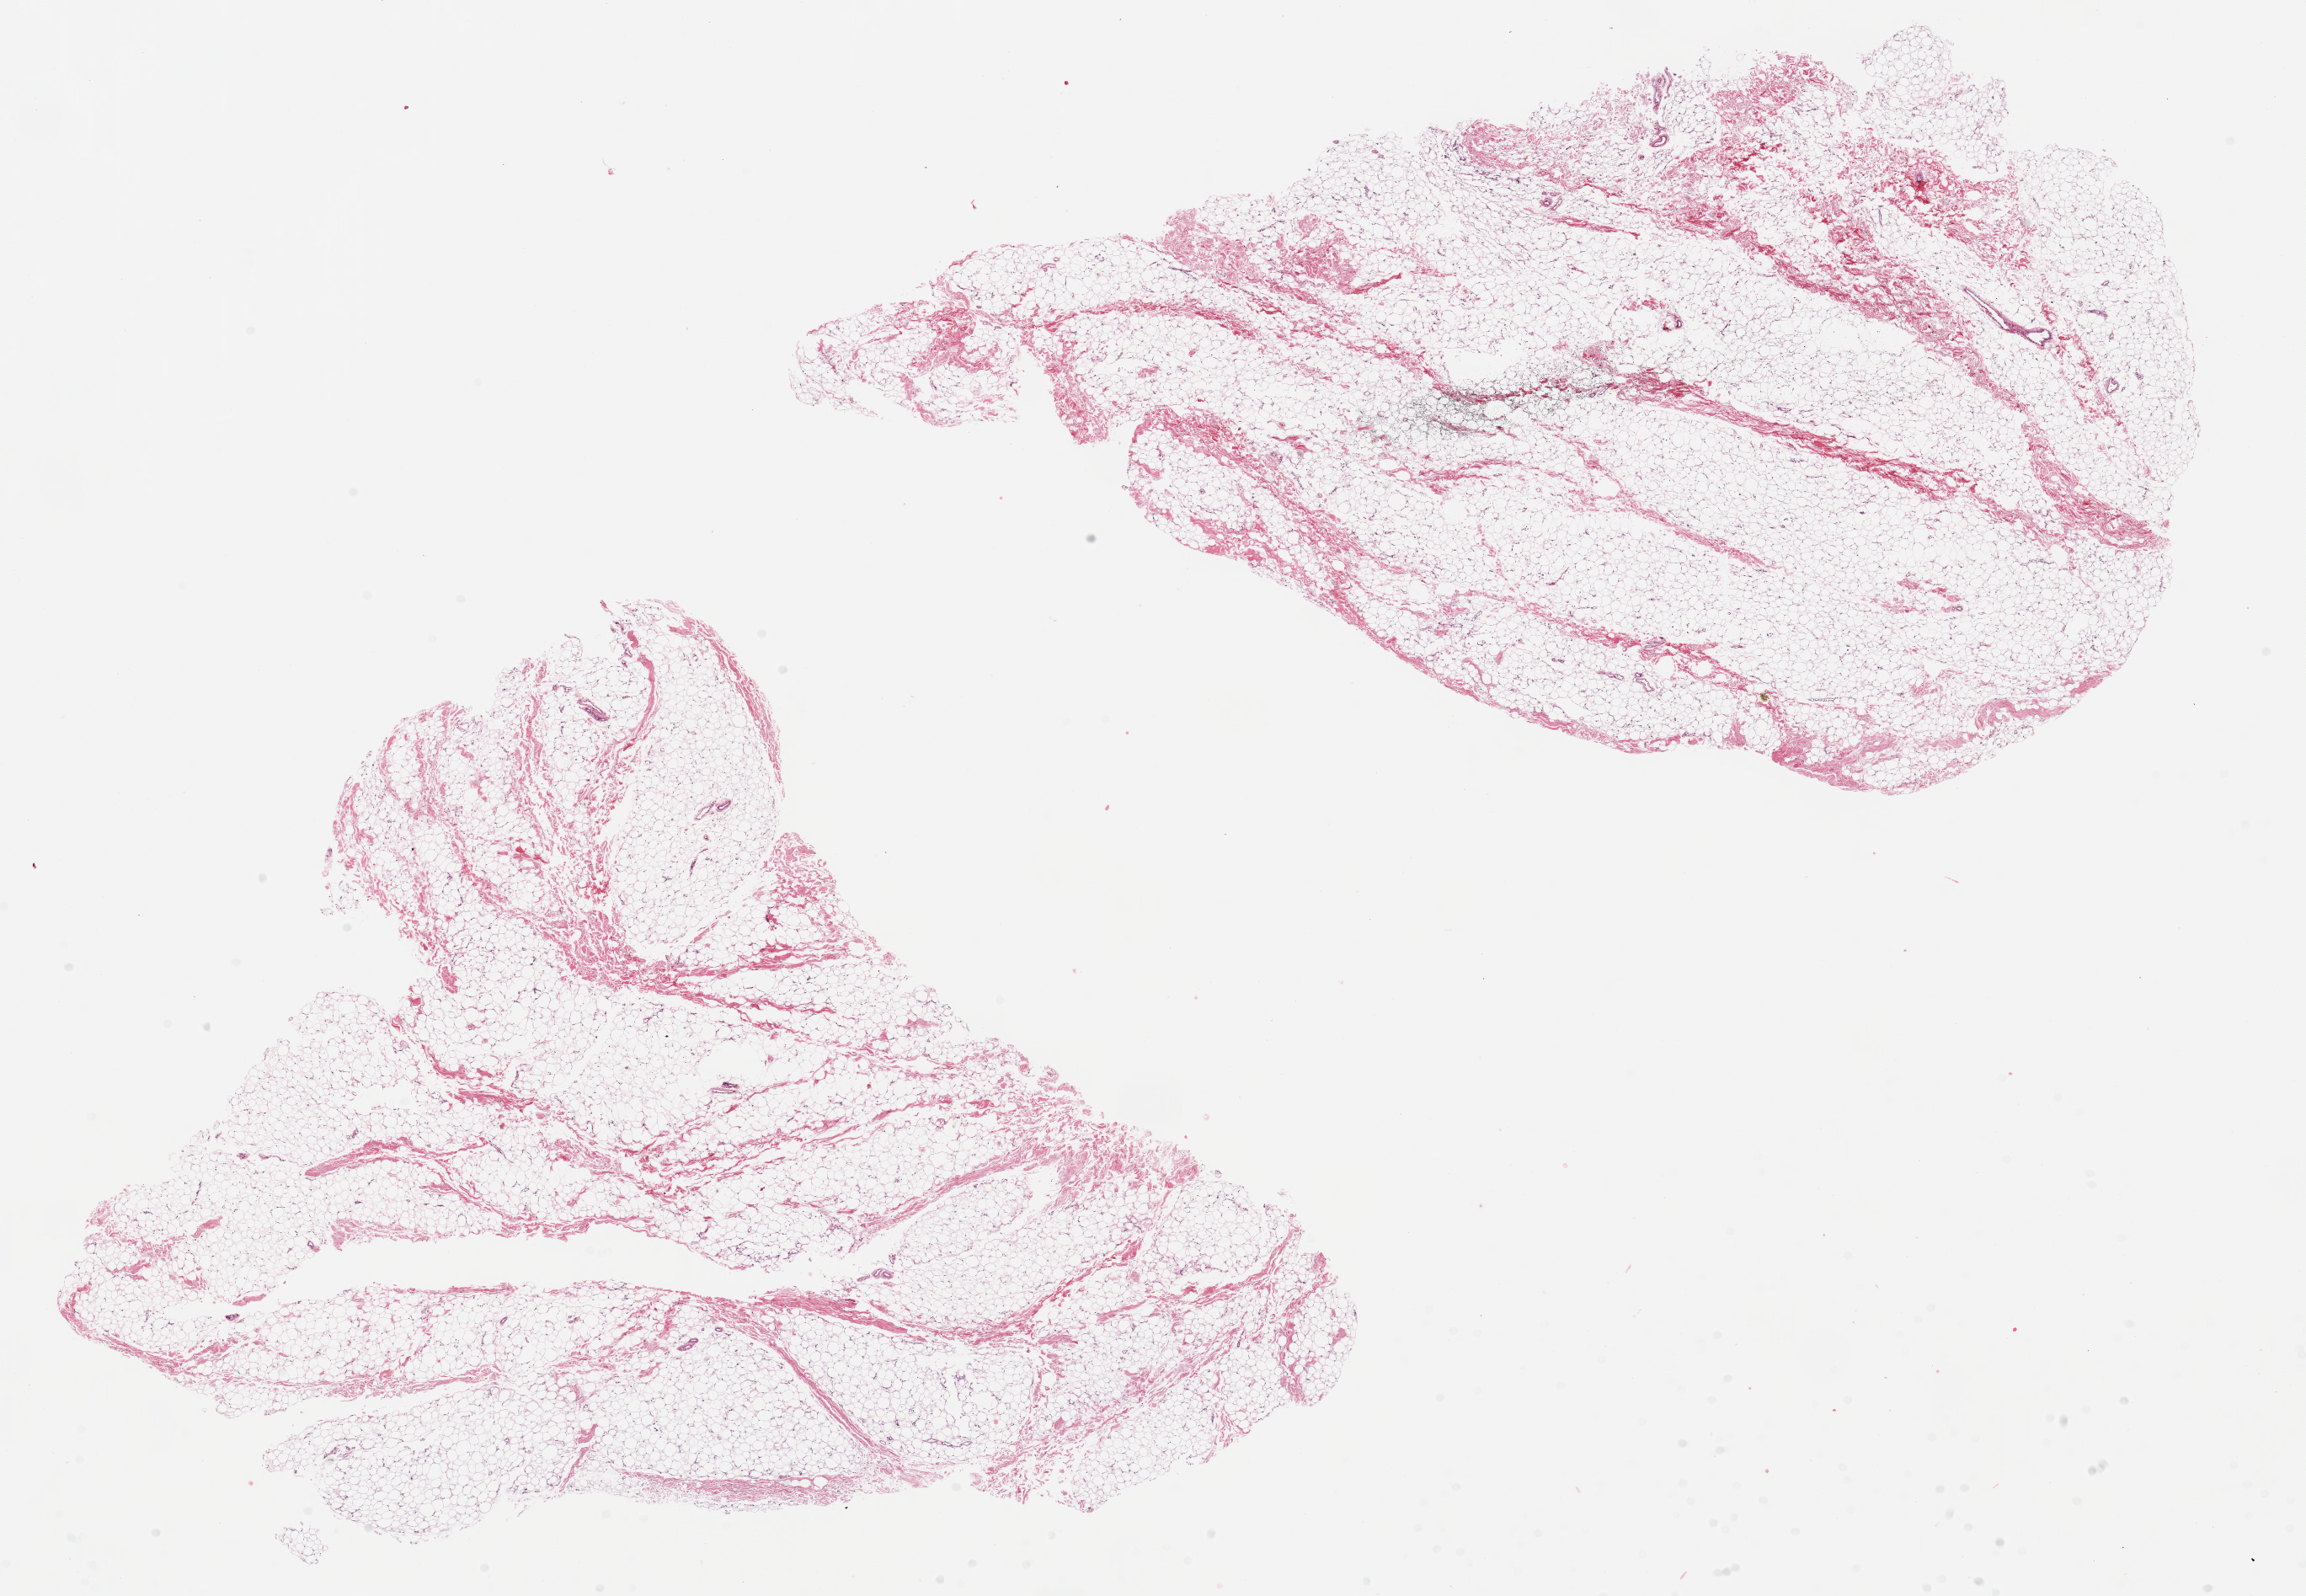
Whole-slide image, H&E stain — low-resolution overview of the scanned area, about 21.7 x 15.0 mm (acquisition: 20x scan); PAXgene-fixed paraffin-embedded (PFPE) section; section of breast (target tissue); tissue donor sample. Donor: male.
Reviewer comment on this tissue sample: 2 pieces, ~10x7.5mm, pure adipose/fibrous tissue, no ductal elements noted.